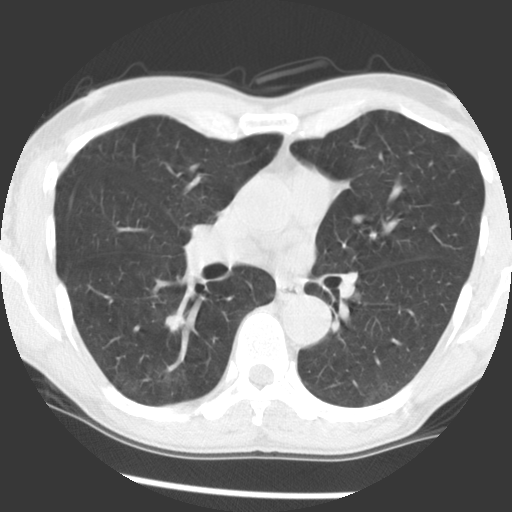
Low-dose screening chest CT, axial slice. Baseline screening round. Lung window (W 1500 / L -600 HU). Male, age 65 years at enrolment. Current smoker at enrolment.
Expert-annotated lung lesion, bounding box (x1, y1, x2, y2) in pixels: (150, 300, 205, 343). The screening reader recorded 2 non-calcified nodules or masses ≥4 mm on this exam (right lower lobe, left lower lobe); which of them this box marks is not recorded. Official screen result: positive, change unspecified: nodule(s) >= 4 mm or enlarging nodule(s), mass(es), or other non-specific abnormalities suspicious for lung cancer. Later outcome: lung cancer diagnosed 774 days after this screen — adenocarcinoma, NOS, right lower lobe, poorly differentiated (G3), stage IA (AJCC 6th edition), 18 mm at pathology.